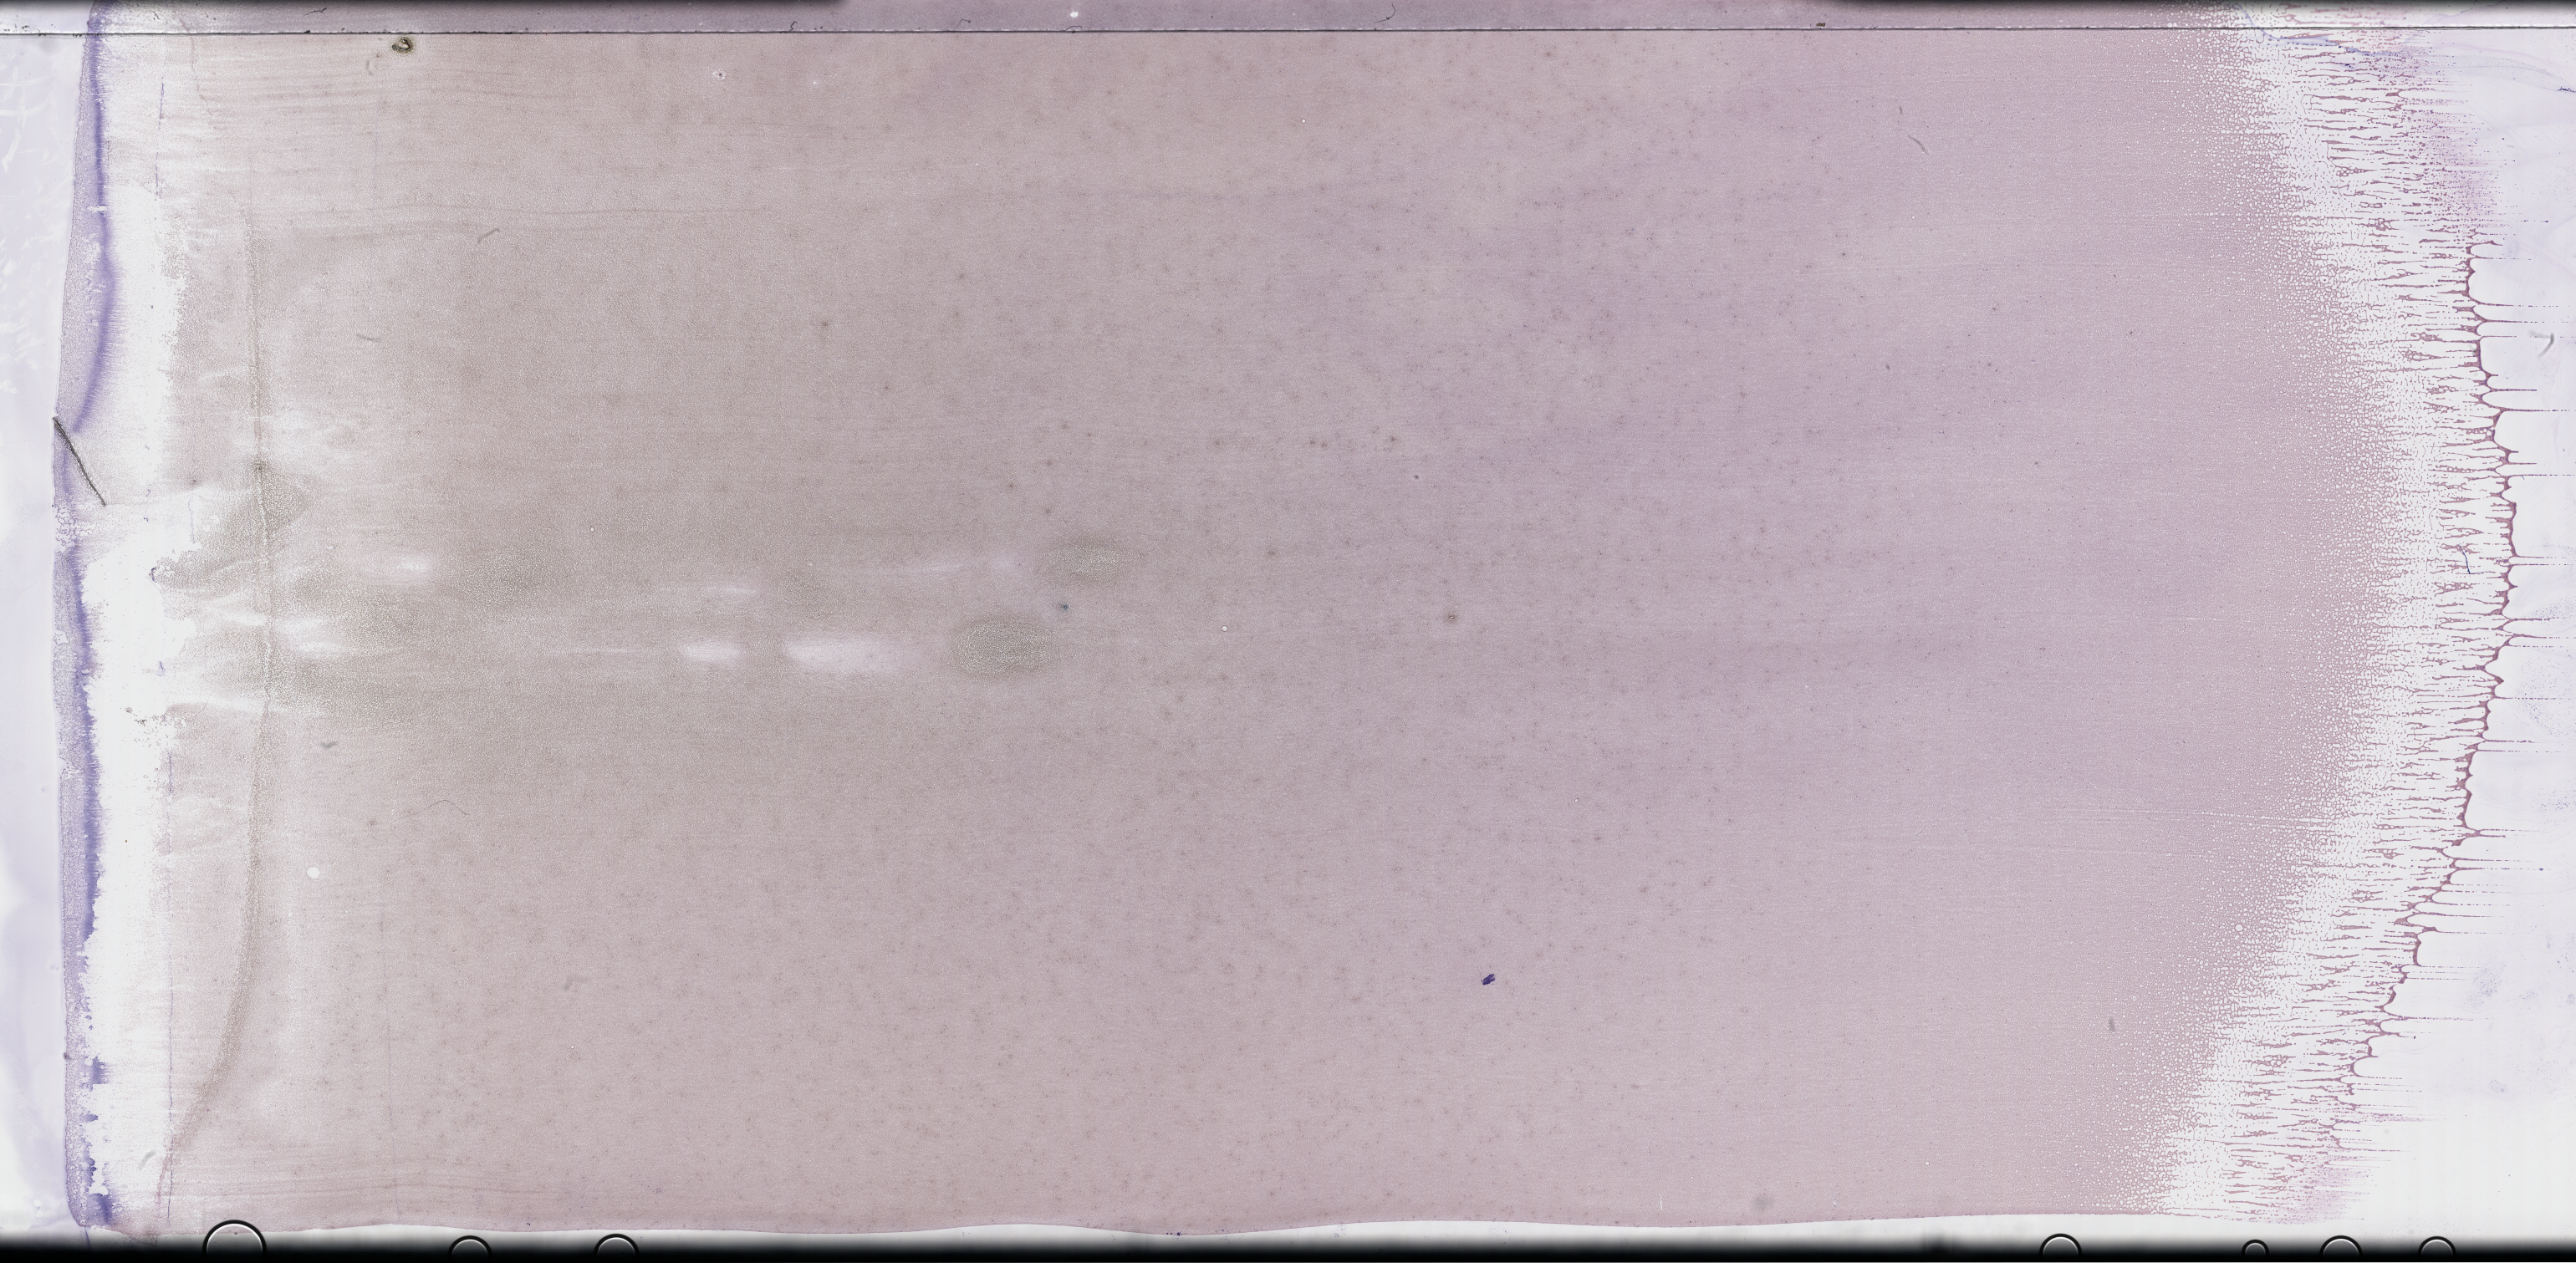
Whole-slide image of a whole blood smear, Wright-Giemsa stain — a low-resolution overview of the entire scanned area, about 49.8 x 24.4 mm. EDTA-anticoagulated smear. Collected on treatment. Patient: male.
* from a patient with: Plasma Cell Myeloma